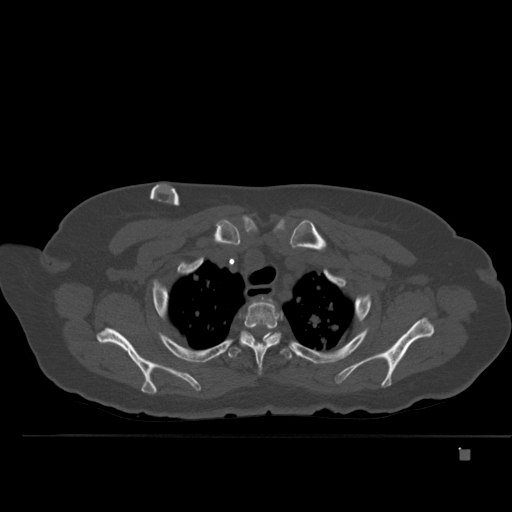
CT including the spine, one axial slice; slice 388 of 477 in the series (ordered by position); bone window (W 1800 / L 400 HU); 512 × 512 image matrix, field of view 422 × 422 mm. Female patient, age 74 years. From the clinical record (not read from this slice): primary cancer: colon.
Structures marked on this image (semi-automatic segmentation, software-assisted and operator-edited):
- T1 vertebra: bounding box [x1, y1, x2, y2] px = [252, 300, 272, 303]
- T2 vertebra: [240, 302, 282, 368]
- T3 vertebra: [228, 331, 292, 359]